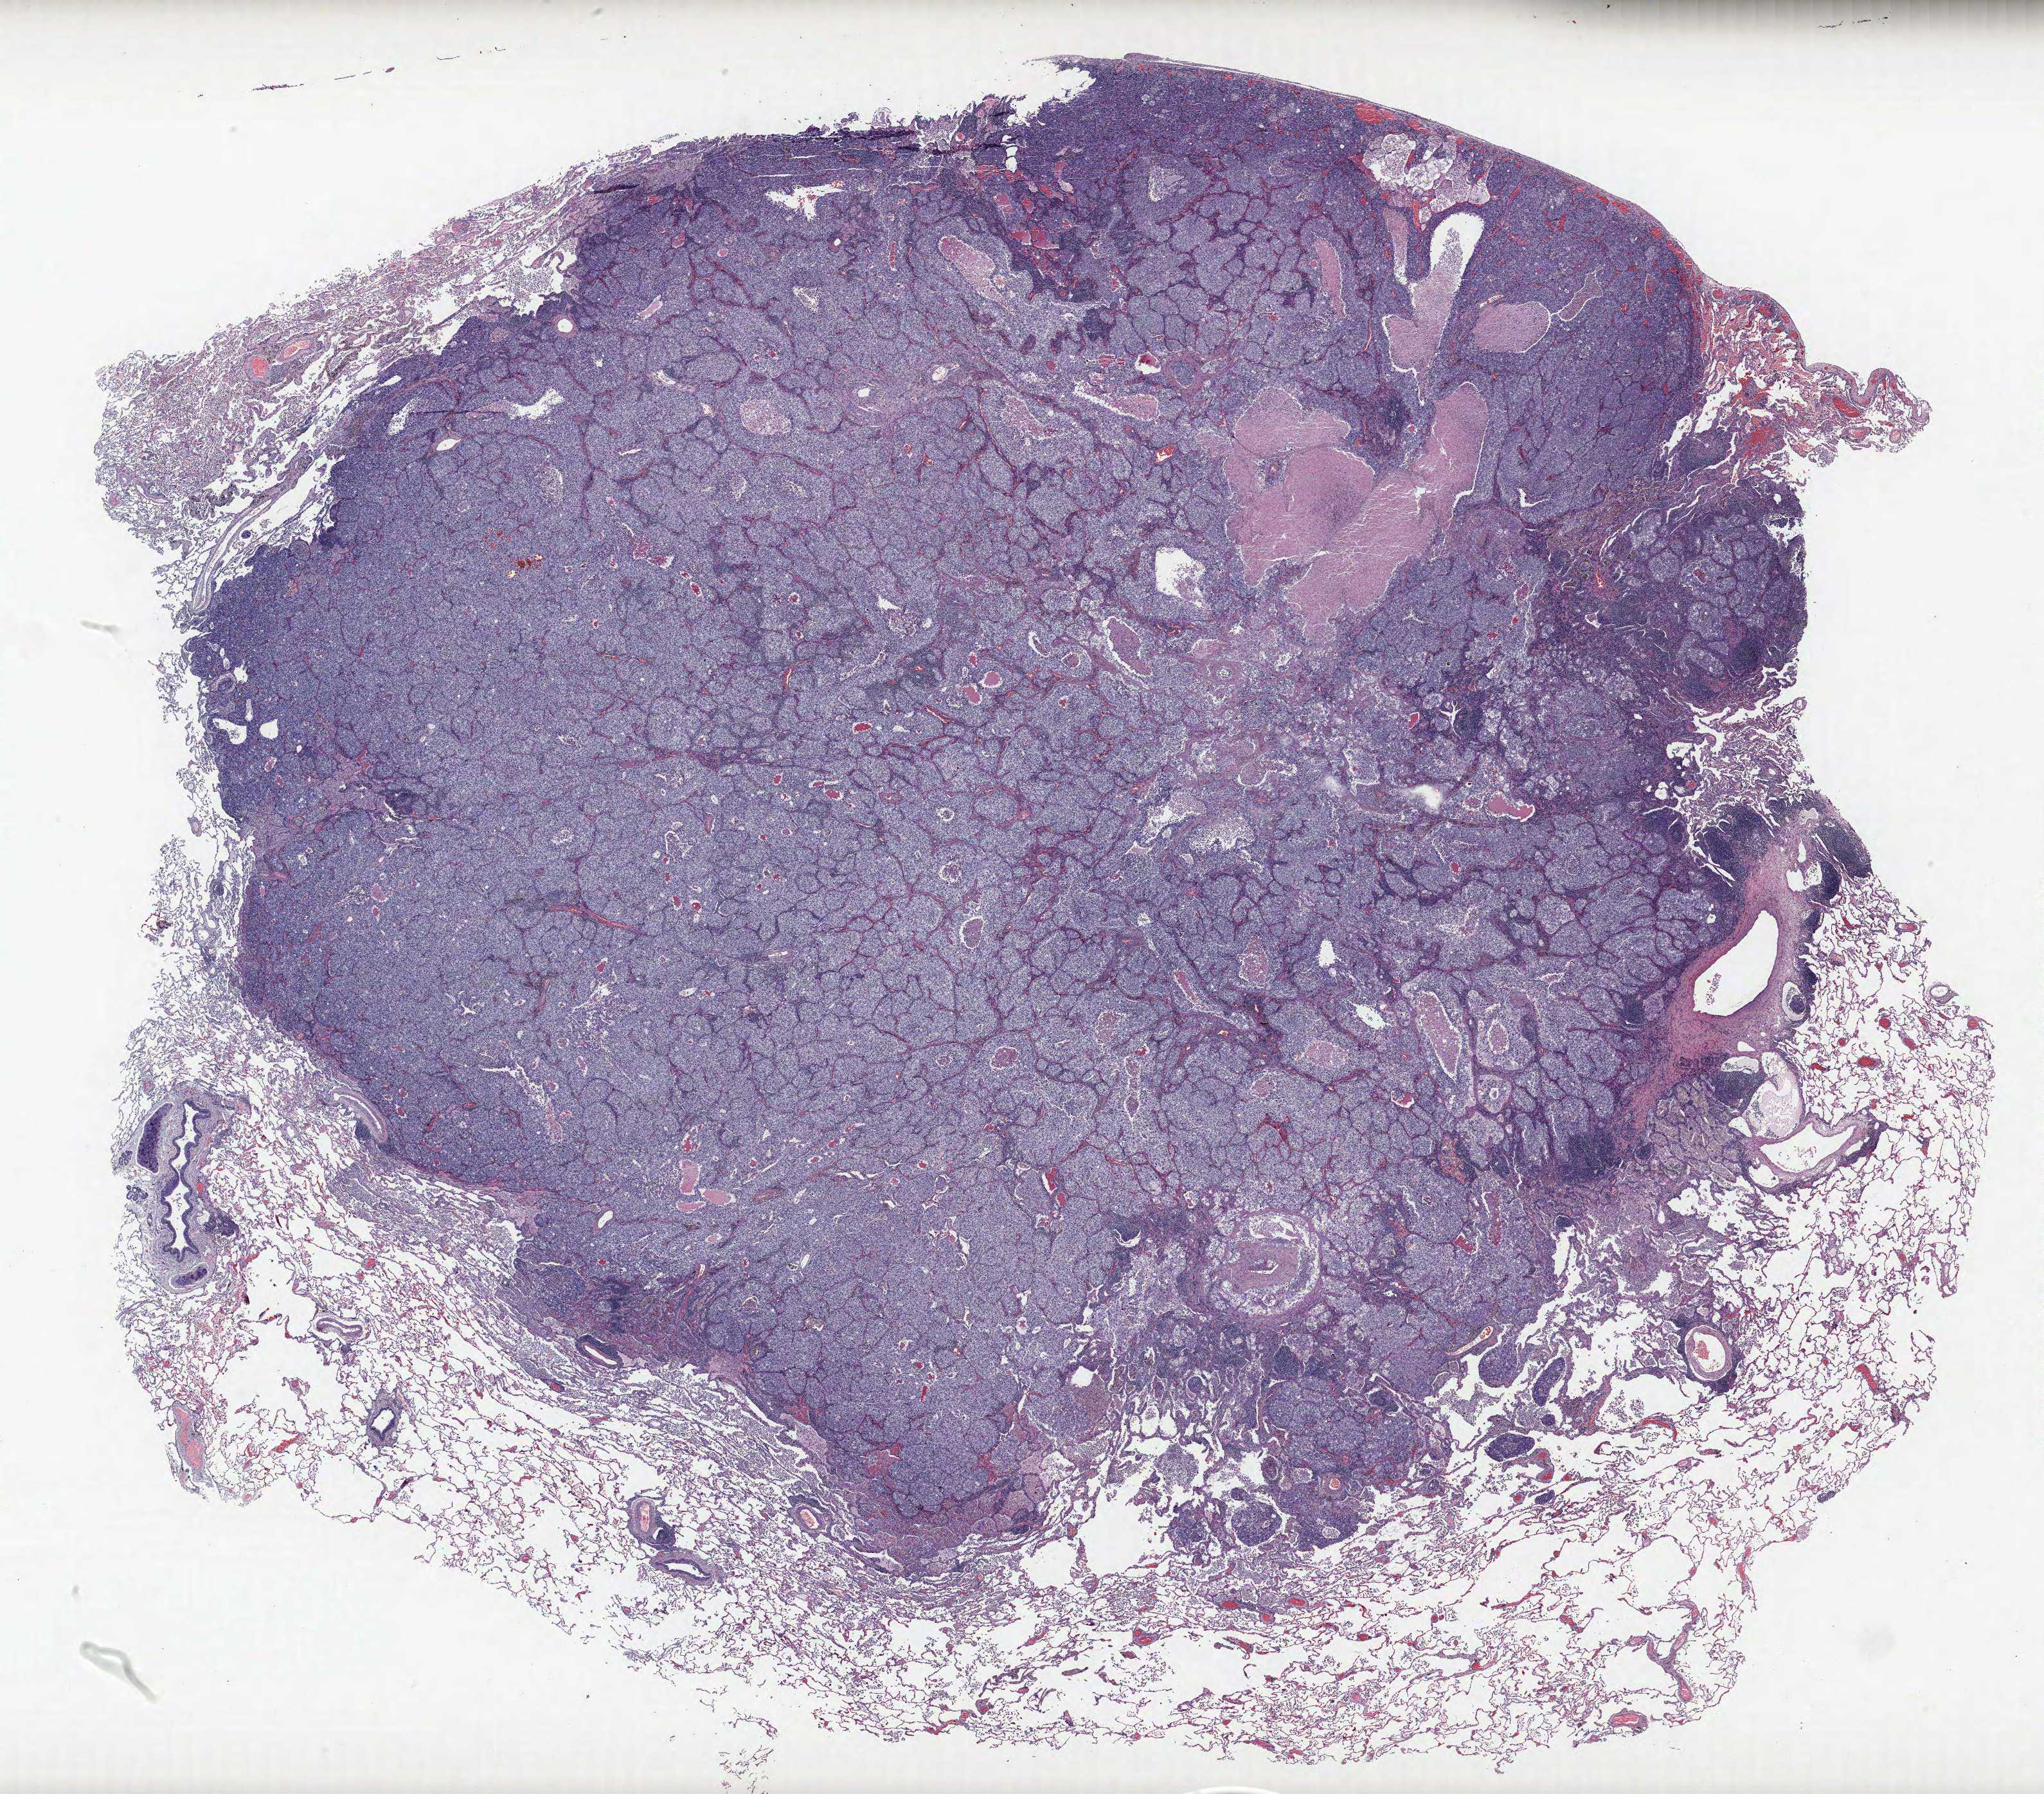
Whole-slide histology image, H&E, whole scanned area (about 25.4 x 22.3 mm) shown as a low-resolution overview, FFPE section, lung tissue. Male patient, aged 62 at enrolment. Current smoker at enrolment. Grade: poorly differentiated (G3).
Tumour size (pathology): 32 mm. Primary tumour location (clinical record): left upper lobe. Participant's lung-cancer diagnosis: Adenocarcinoma, NOS (ICD-O-3 8140/3). Stage (AJCC 6th edition): IB.